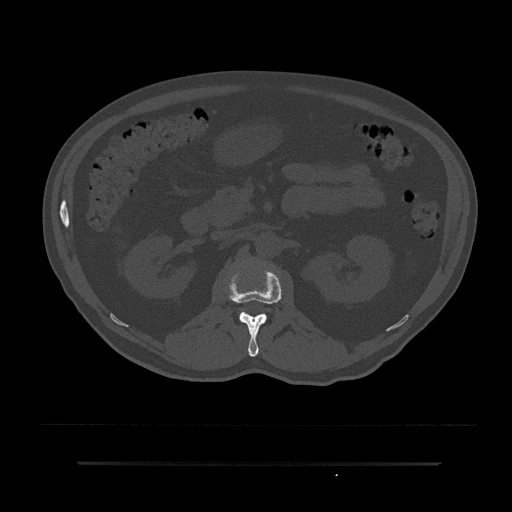
CT including the spine, one axial slice; position 122 of 797 along the scan axis; reconstruction kernel Br40s/3; 120 kVp; bone window (W 1800 / L 400 HU); 512 × 512 image matrix, field of view 464 × 464 mm. Male patient, age 59 years. From the clinical record (not read from this slice): primary cancer: bile ducts; vertebrae with lytic lesions (as recorded): T10.
Structures marked on this image (semi-automatic segmentation, software-assisted and operator-edited):
- L1 vertebra: box from (x=227, y=267) to (x=283, y=357) px